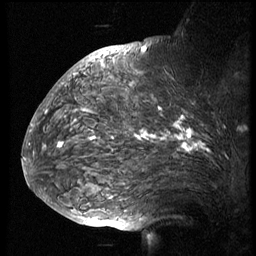
Breast MRI (dynamic contrast-enhanced), one sagittal slice. Position 45 of 74 along the scan axis. 3 images stored at this slice position (order not interpretable as contrast timing). 1.5 T. TE 4.2 ms, TR 8.9 ms. 256 × 256 image matrix, field of view 200 × 200 mm. Patient: female, 57 years. Case-level facts recorded for this patient, not image findings: setting: breast cancer imaged before/during neoadjuvant chemotherapy; receptor status: HER2-positive.
Outlined on this slice (semi-automatically segmented with operator editing):
- analysis volume of interest (the breast-tissue region the enhancement analysis was run in; not a lesion): bounding box (x1, y1, x2, y2) in pixels: (51, 67, 247, 173)
- tumour enhancement mask (voxels above the 140 % enhancement threshold inside the analysis volume of interest): (60, 109, 210, 153)